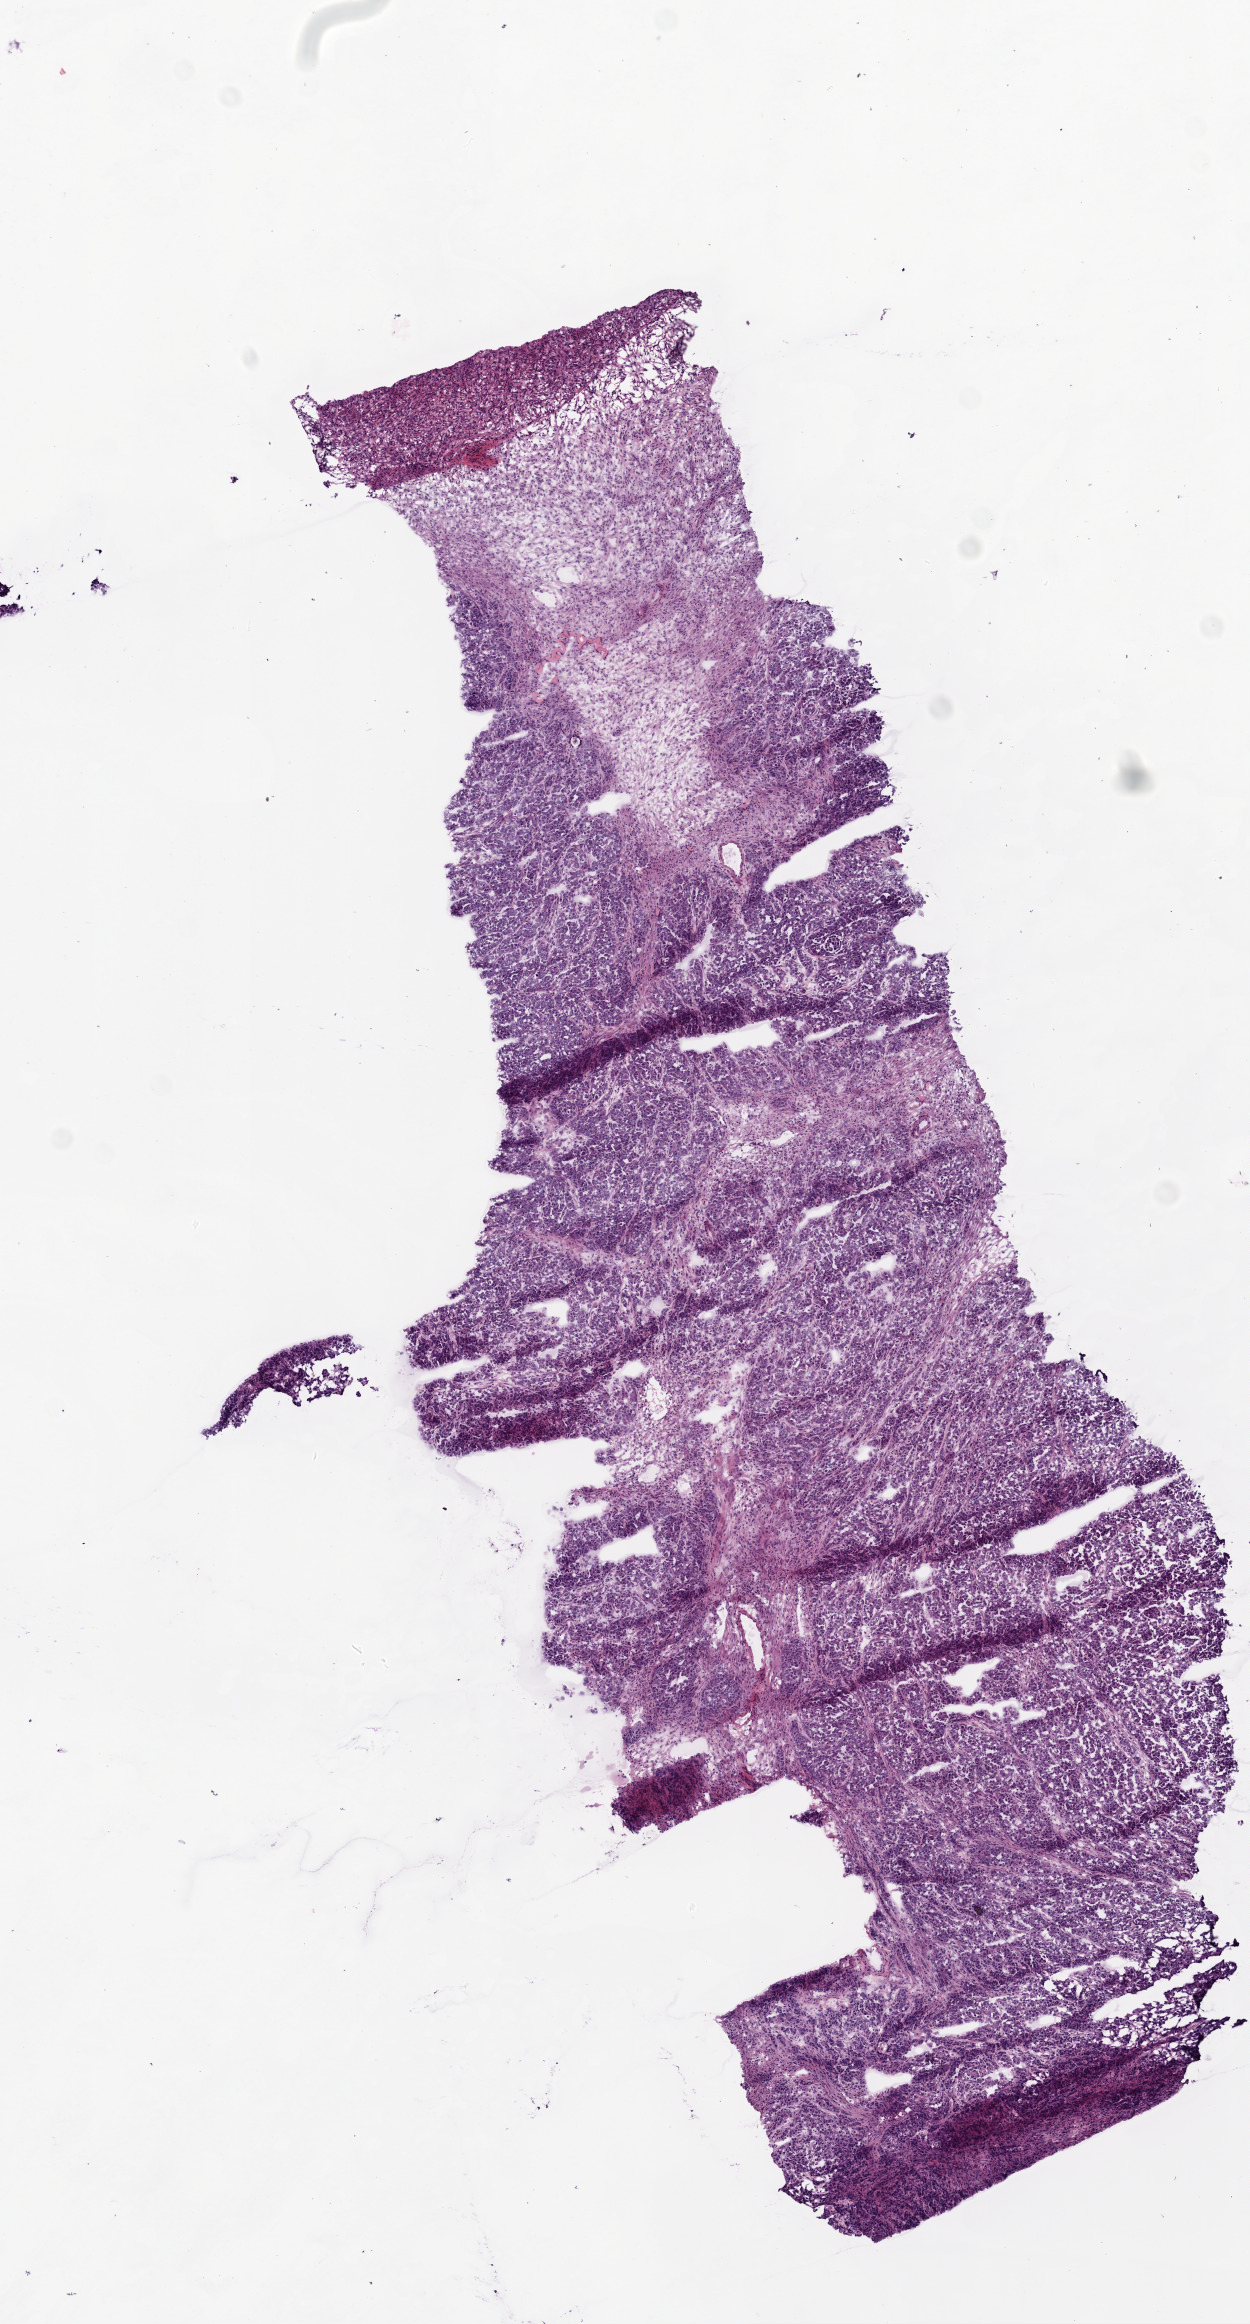
Whole-slide histology image, H&E-stained — low-resolution overview of the scanned area, about 5.0 x 9.3 mm (acquisition: 20x scan); frozen section from the bottom of the tissue portion; ovary, primary tumour sample. Female, age 45 years at initial diagnosis. Histologic grade: G3 (poorly differentiated). Slide review estimates, as recorded: tumour cells 85%, tumour nuclei 85%, normal cells 1%, stromal cells 14%, necrosis 0%.
* laterality: right
* histologic diagnosis: Serous cystadenocarcinoma, NOS
* FIGO stage: IV